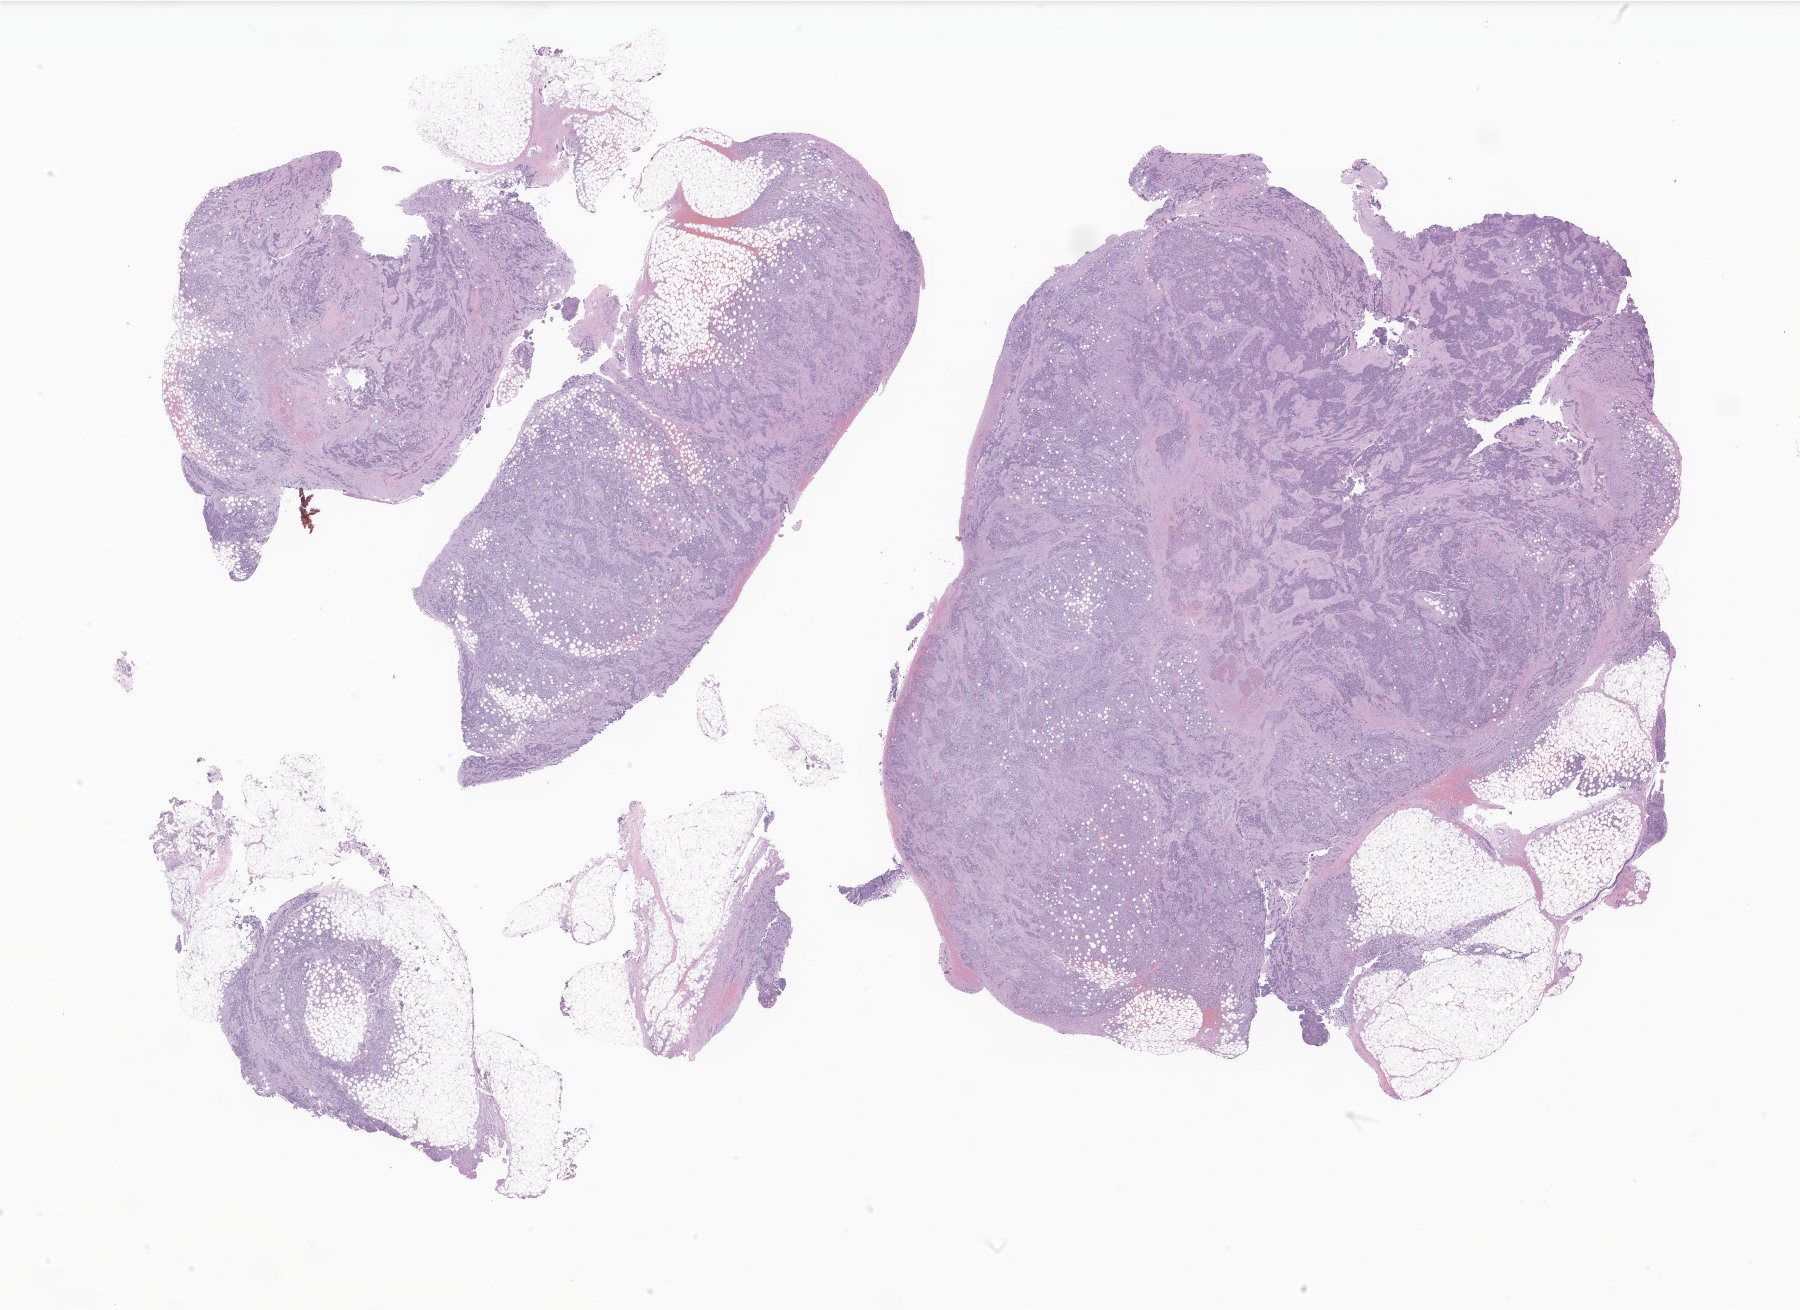
Digitized haematoxylin and eosin-stained section of tumor tissue — shown as a low-resolution overview of the whole scanned area (about 30.4 x 22.1 mm), formalin-fixed paraffin-embedded section. Patient female; age 190 months (15 years 10 months).
Recorded diagnosis: Alveolar rhabdomyosarcoma.